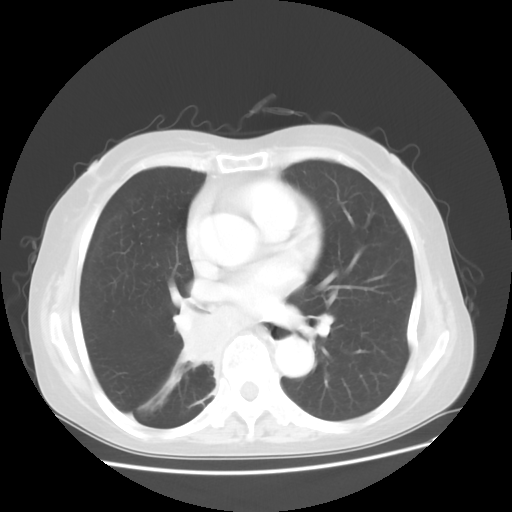
Chest CT, one axial slice; lung window (W 1500 / L -600 HU); 512 × 512 image matrix. Female patient, age 63 years. From the clinical record (not read from this slice): clinical TNM (as recorded): T2 N3 M1b; histopathological grade: G3.
Structures marked on this image (rectangle marked by the reading radiologist):
- lung tumour (recorded histology: small cell carcinoma): bounding box [x1, y1, x2, y2] px = [175, 306, 221, 370]